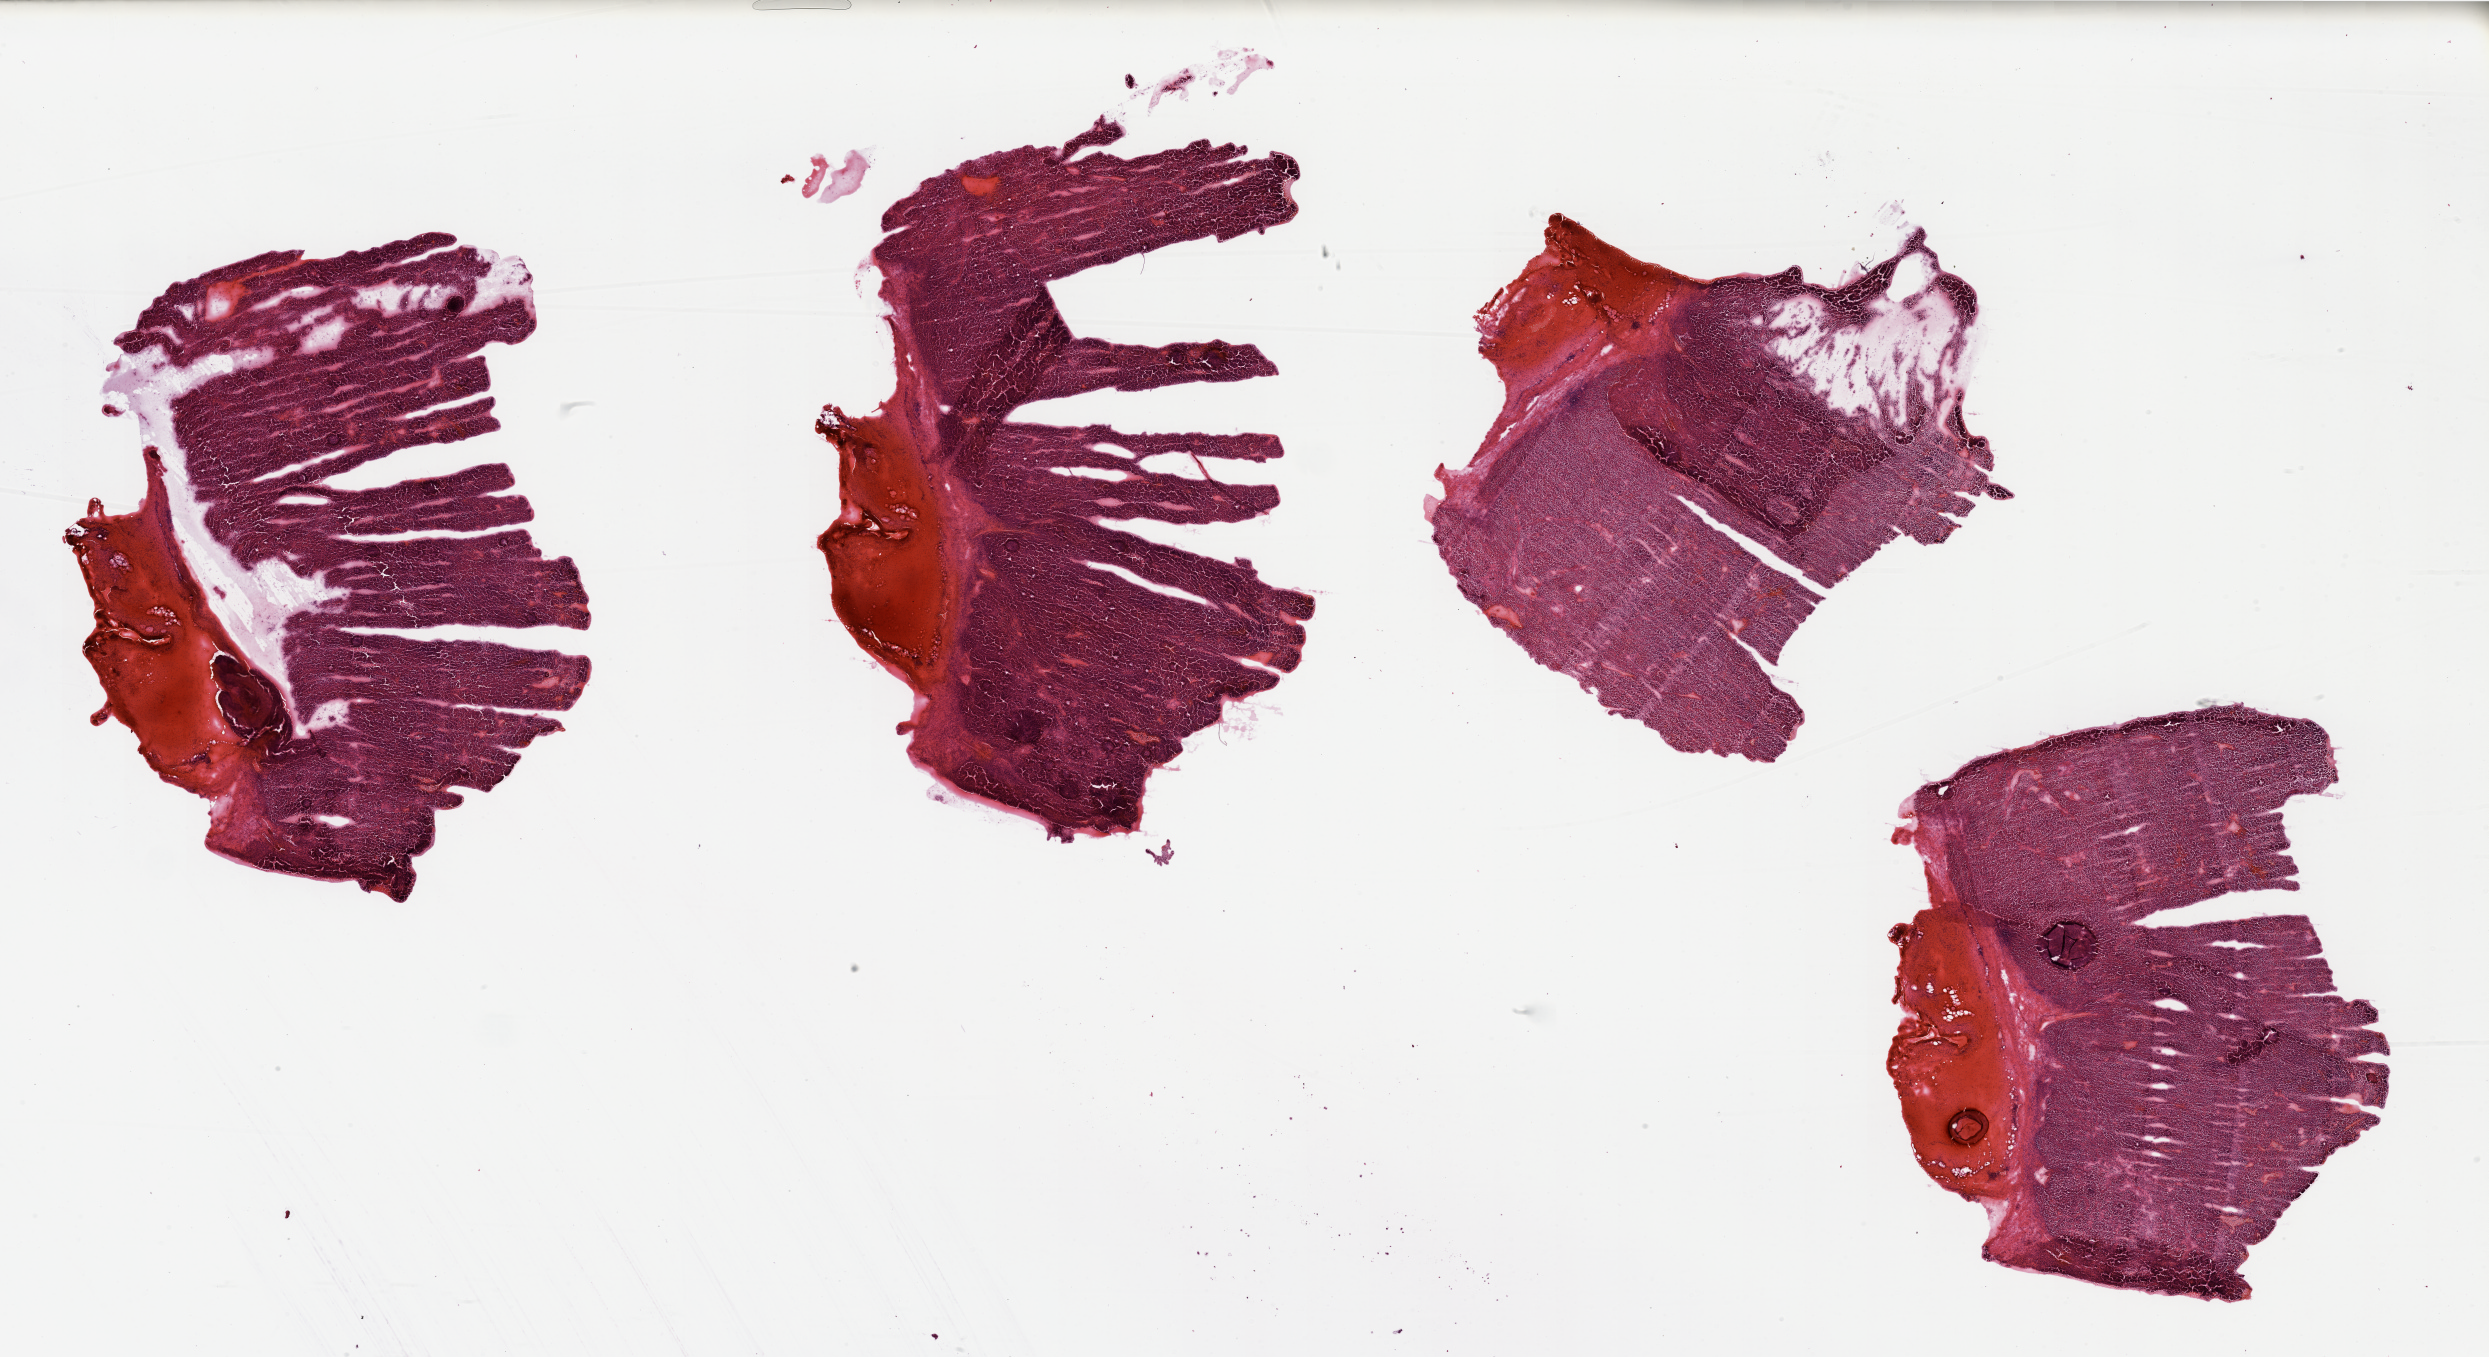
Digitized H&E tissue section (whole slide) — whole scanned area (about 39.4 x 21.5 mm, from a 20x scan) shown as a low-resolution overview, tumour tissue sample, sampled site: kidney. Male, 68 y/o.
Histologic diagnosis: Renal cell carcinoma, NOS.